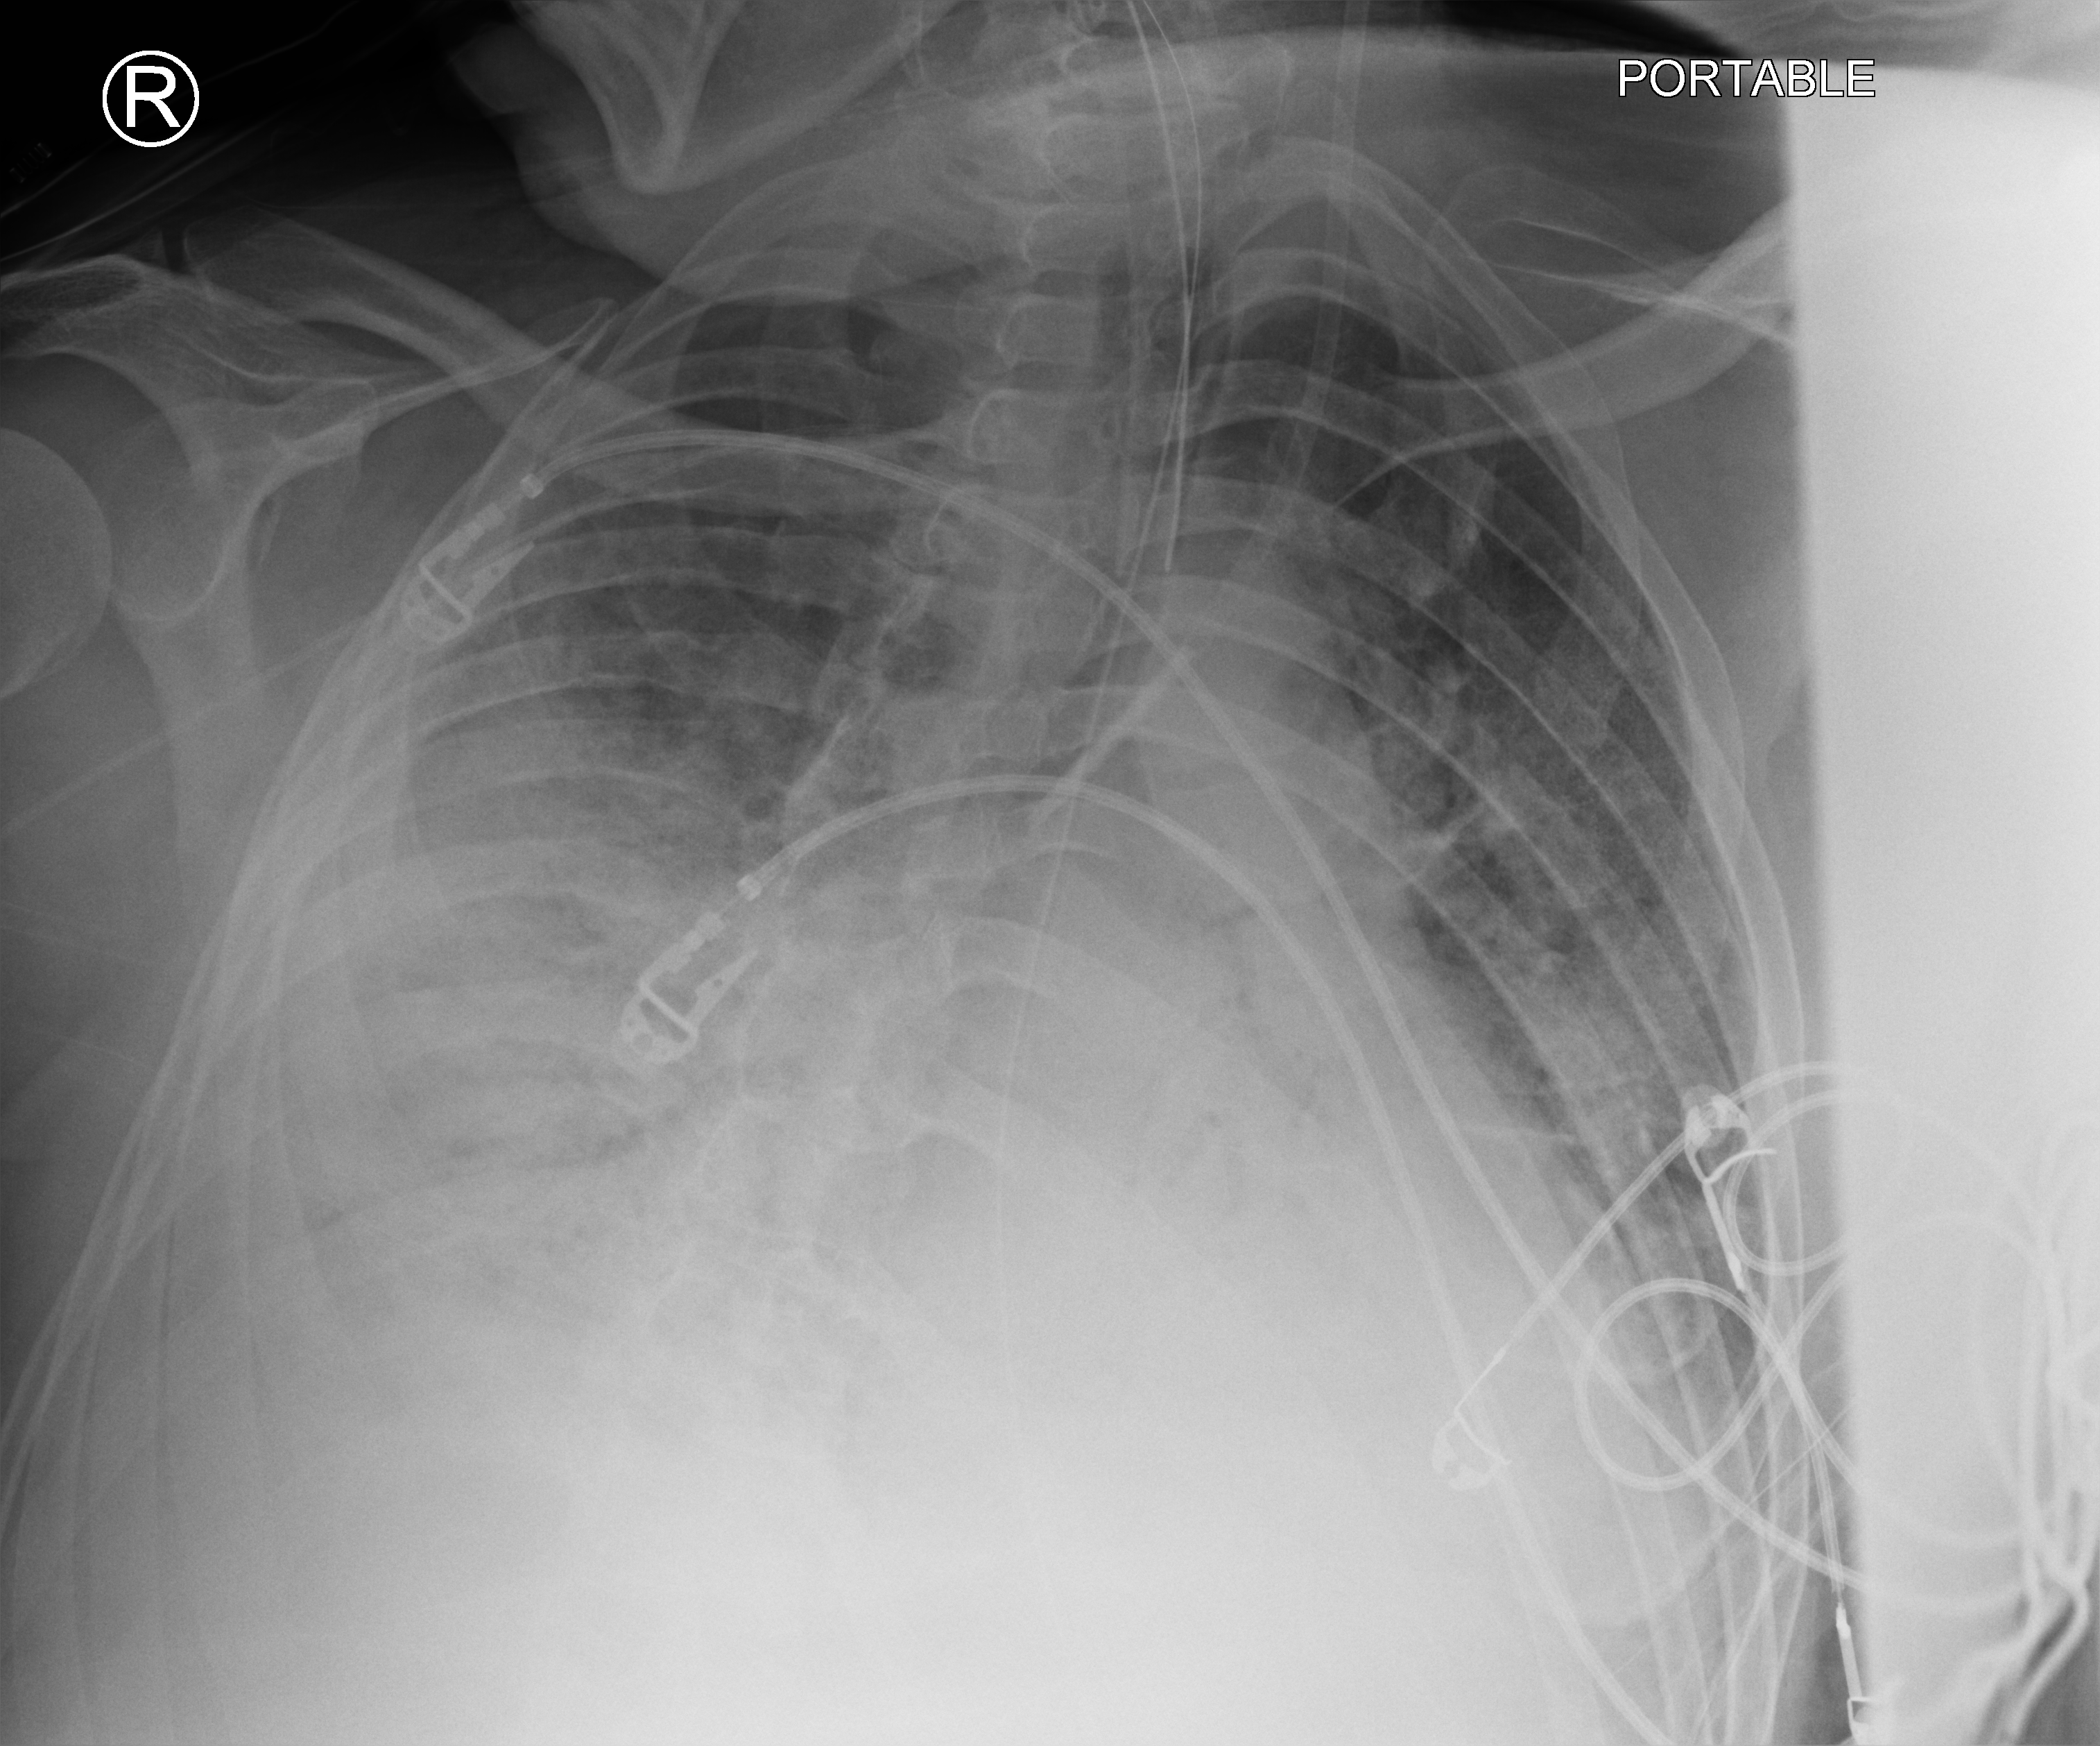
Portable chest radiograph. Patient hospitalised with COVID-19; male, aged 18–59 years.
Hospital-stay facts (about this admission, not read from this image; timing relative to this image not recorded): mechanically ventilated during this hospital stay: yes.